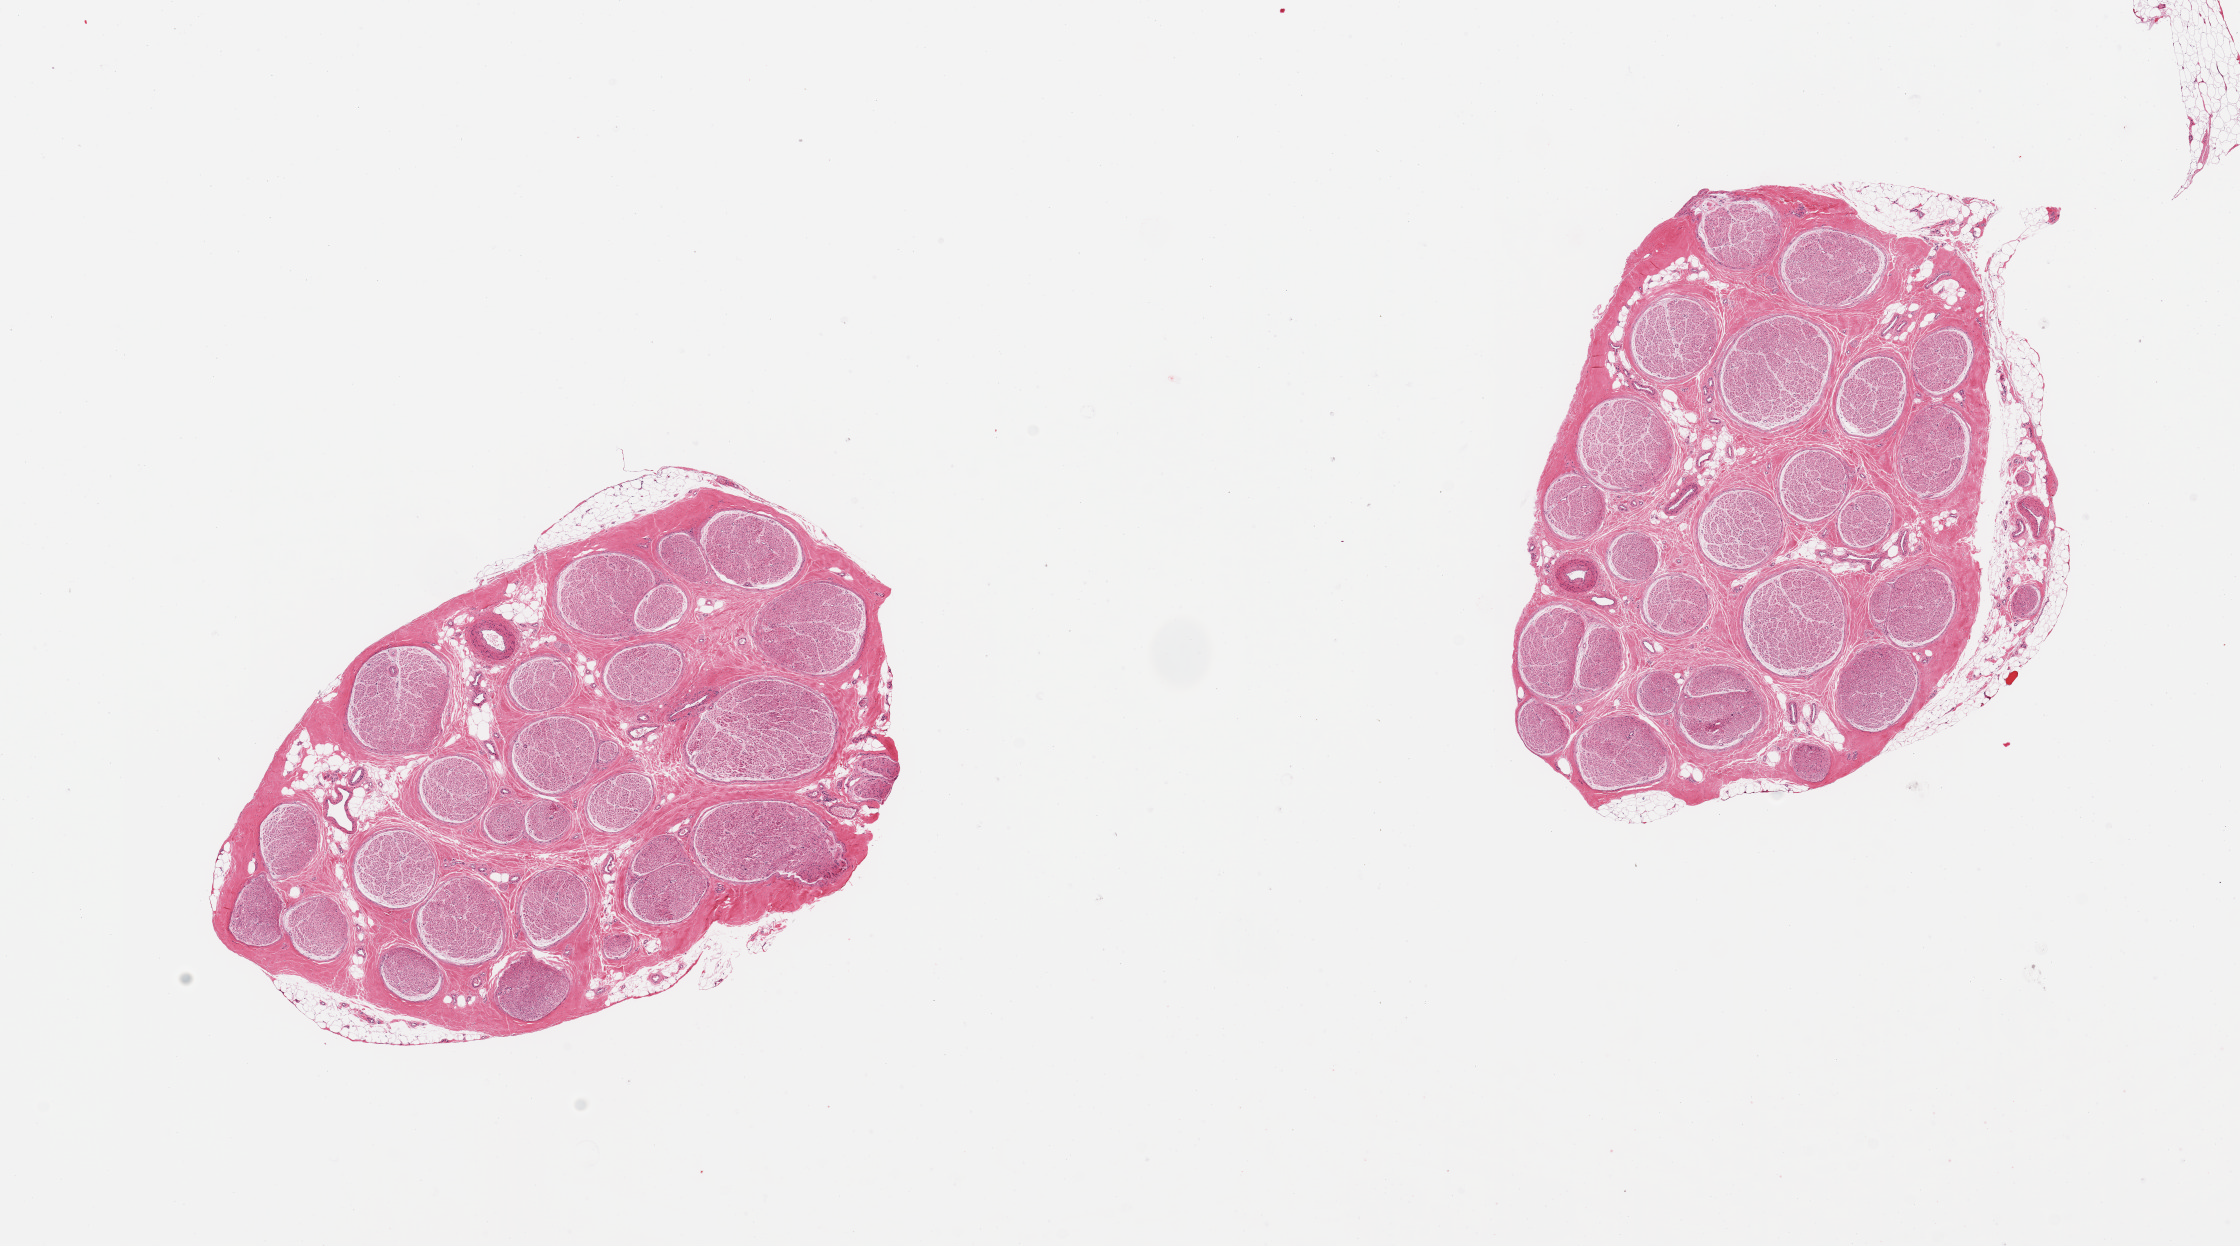
Digitized H&E-stained section, a low-resolution overview of the entire scanned area, about 17.7 x 9.9 mm (acquisition: 20x scan). PAXgene-fixed, paraffin-embedded tissue. Target tissue: tibial nerve. Donor tissue sample.
Reviewer comment on this tissue sample: 2 pieces; well trimmed.